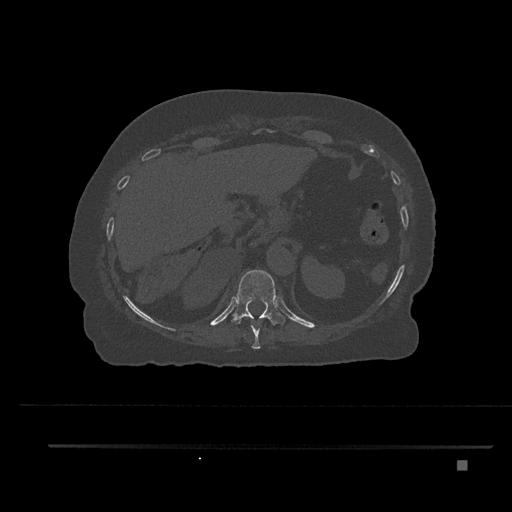
CT including the spine, one axial slice. Slice 322 of 797 in the series (ordered by position). 120 kVp. Bone window (W 1800 / L 400 HU). 0.5 mm slice thickness. 512 × 512 image matrix, field of view 437 × 437 mm. Female patient, age 76 years. From the clinical record (not read from this slice): primary cancer: lung; vertebrae with lytic lesions (as recorded): T11, L3.
Annotated regions visible in this slice (semi-automatic segmentation, software-assisted and operator-edited):
- T10 vertebra: bounding box [x1, y1, x2, y2] px = [250, 318, 261, 349]
- T11 vertebra: [232, 270, 285, 325]